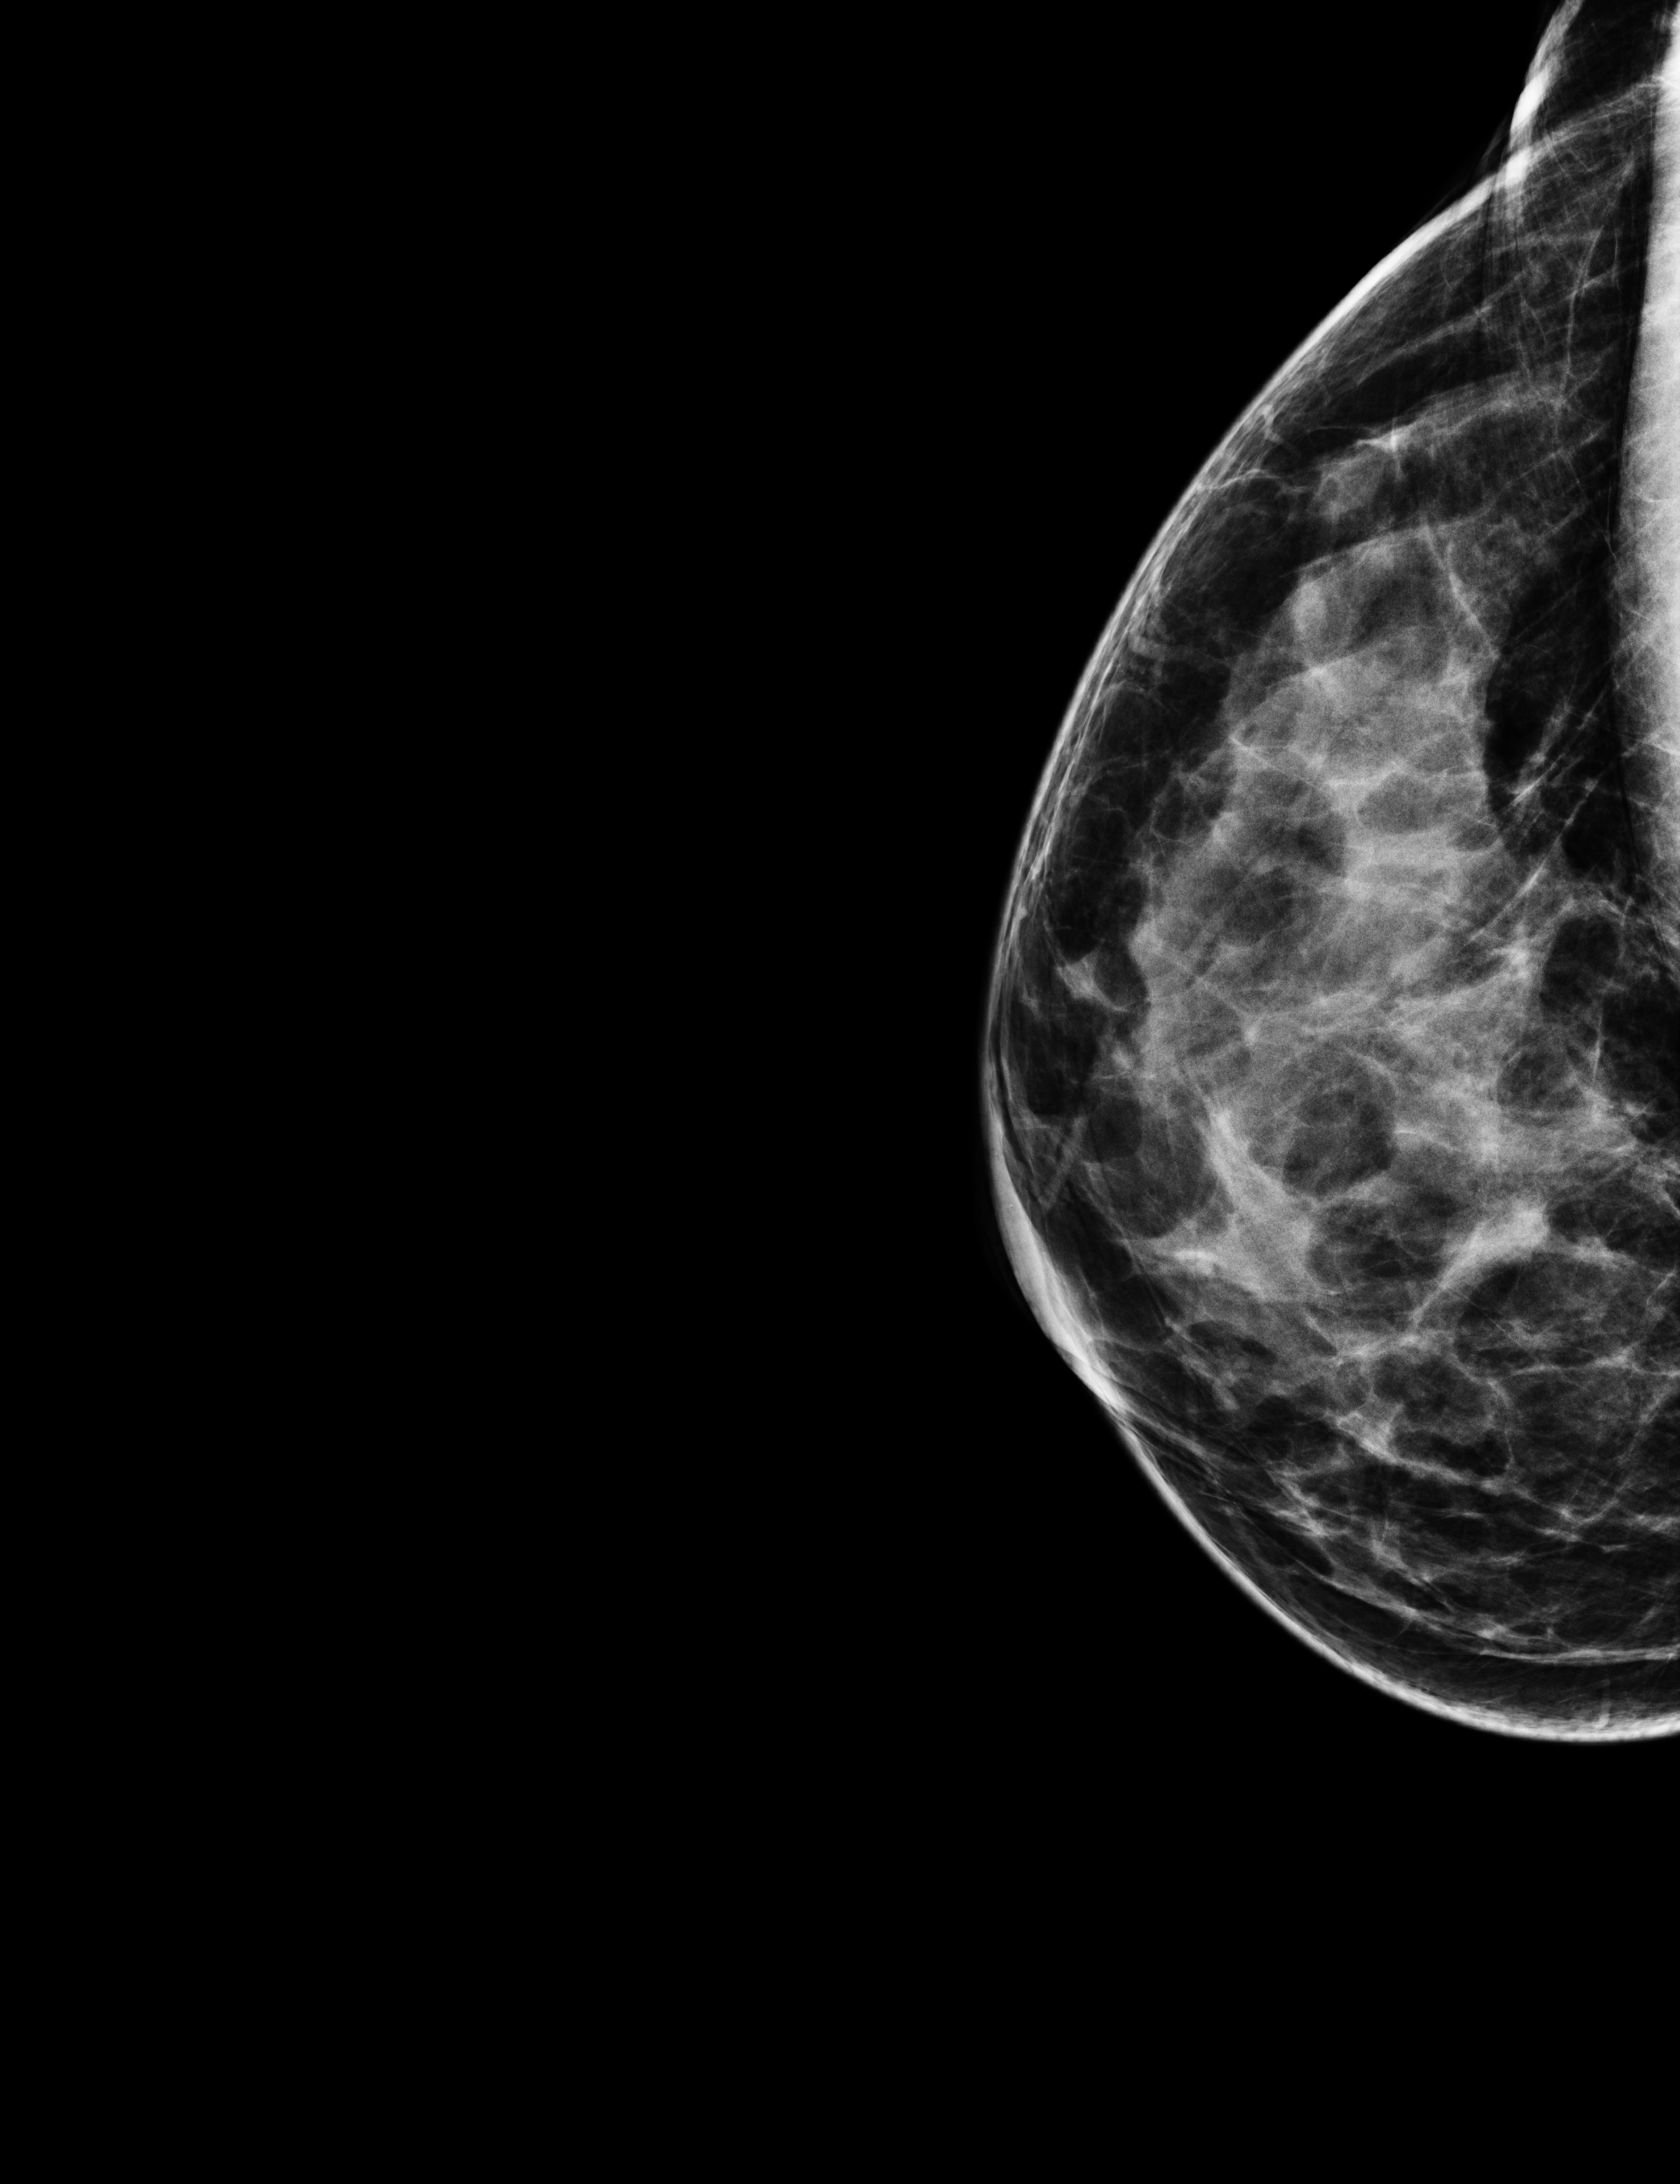
Digital mammogram (FFDM), right breast, laterally exaggerated craniocaudal (XCCL) view, annual screening mammography examination, compressed breast thickness 56 mm. Patient aged 44 years (female).
BI-RADS breast density category at the screening exam (both breasts, scale 1–4): 4. Final BI-RADS category for the screening round (tomosynthesis exam, both breasts): category 1. Recall: no recall after this screen.